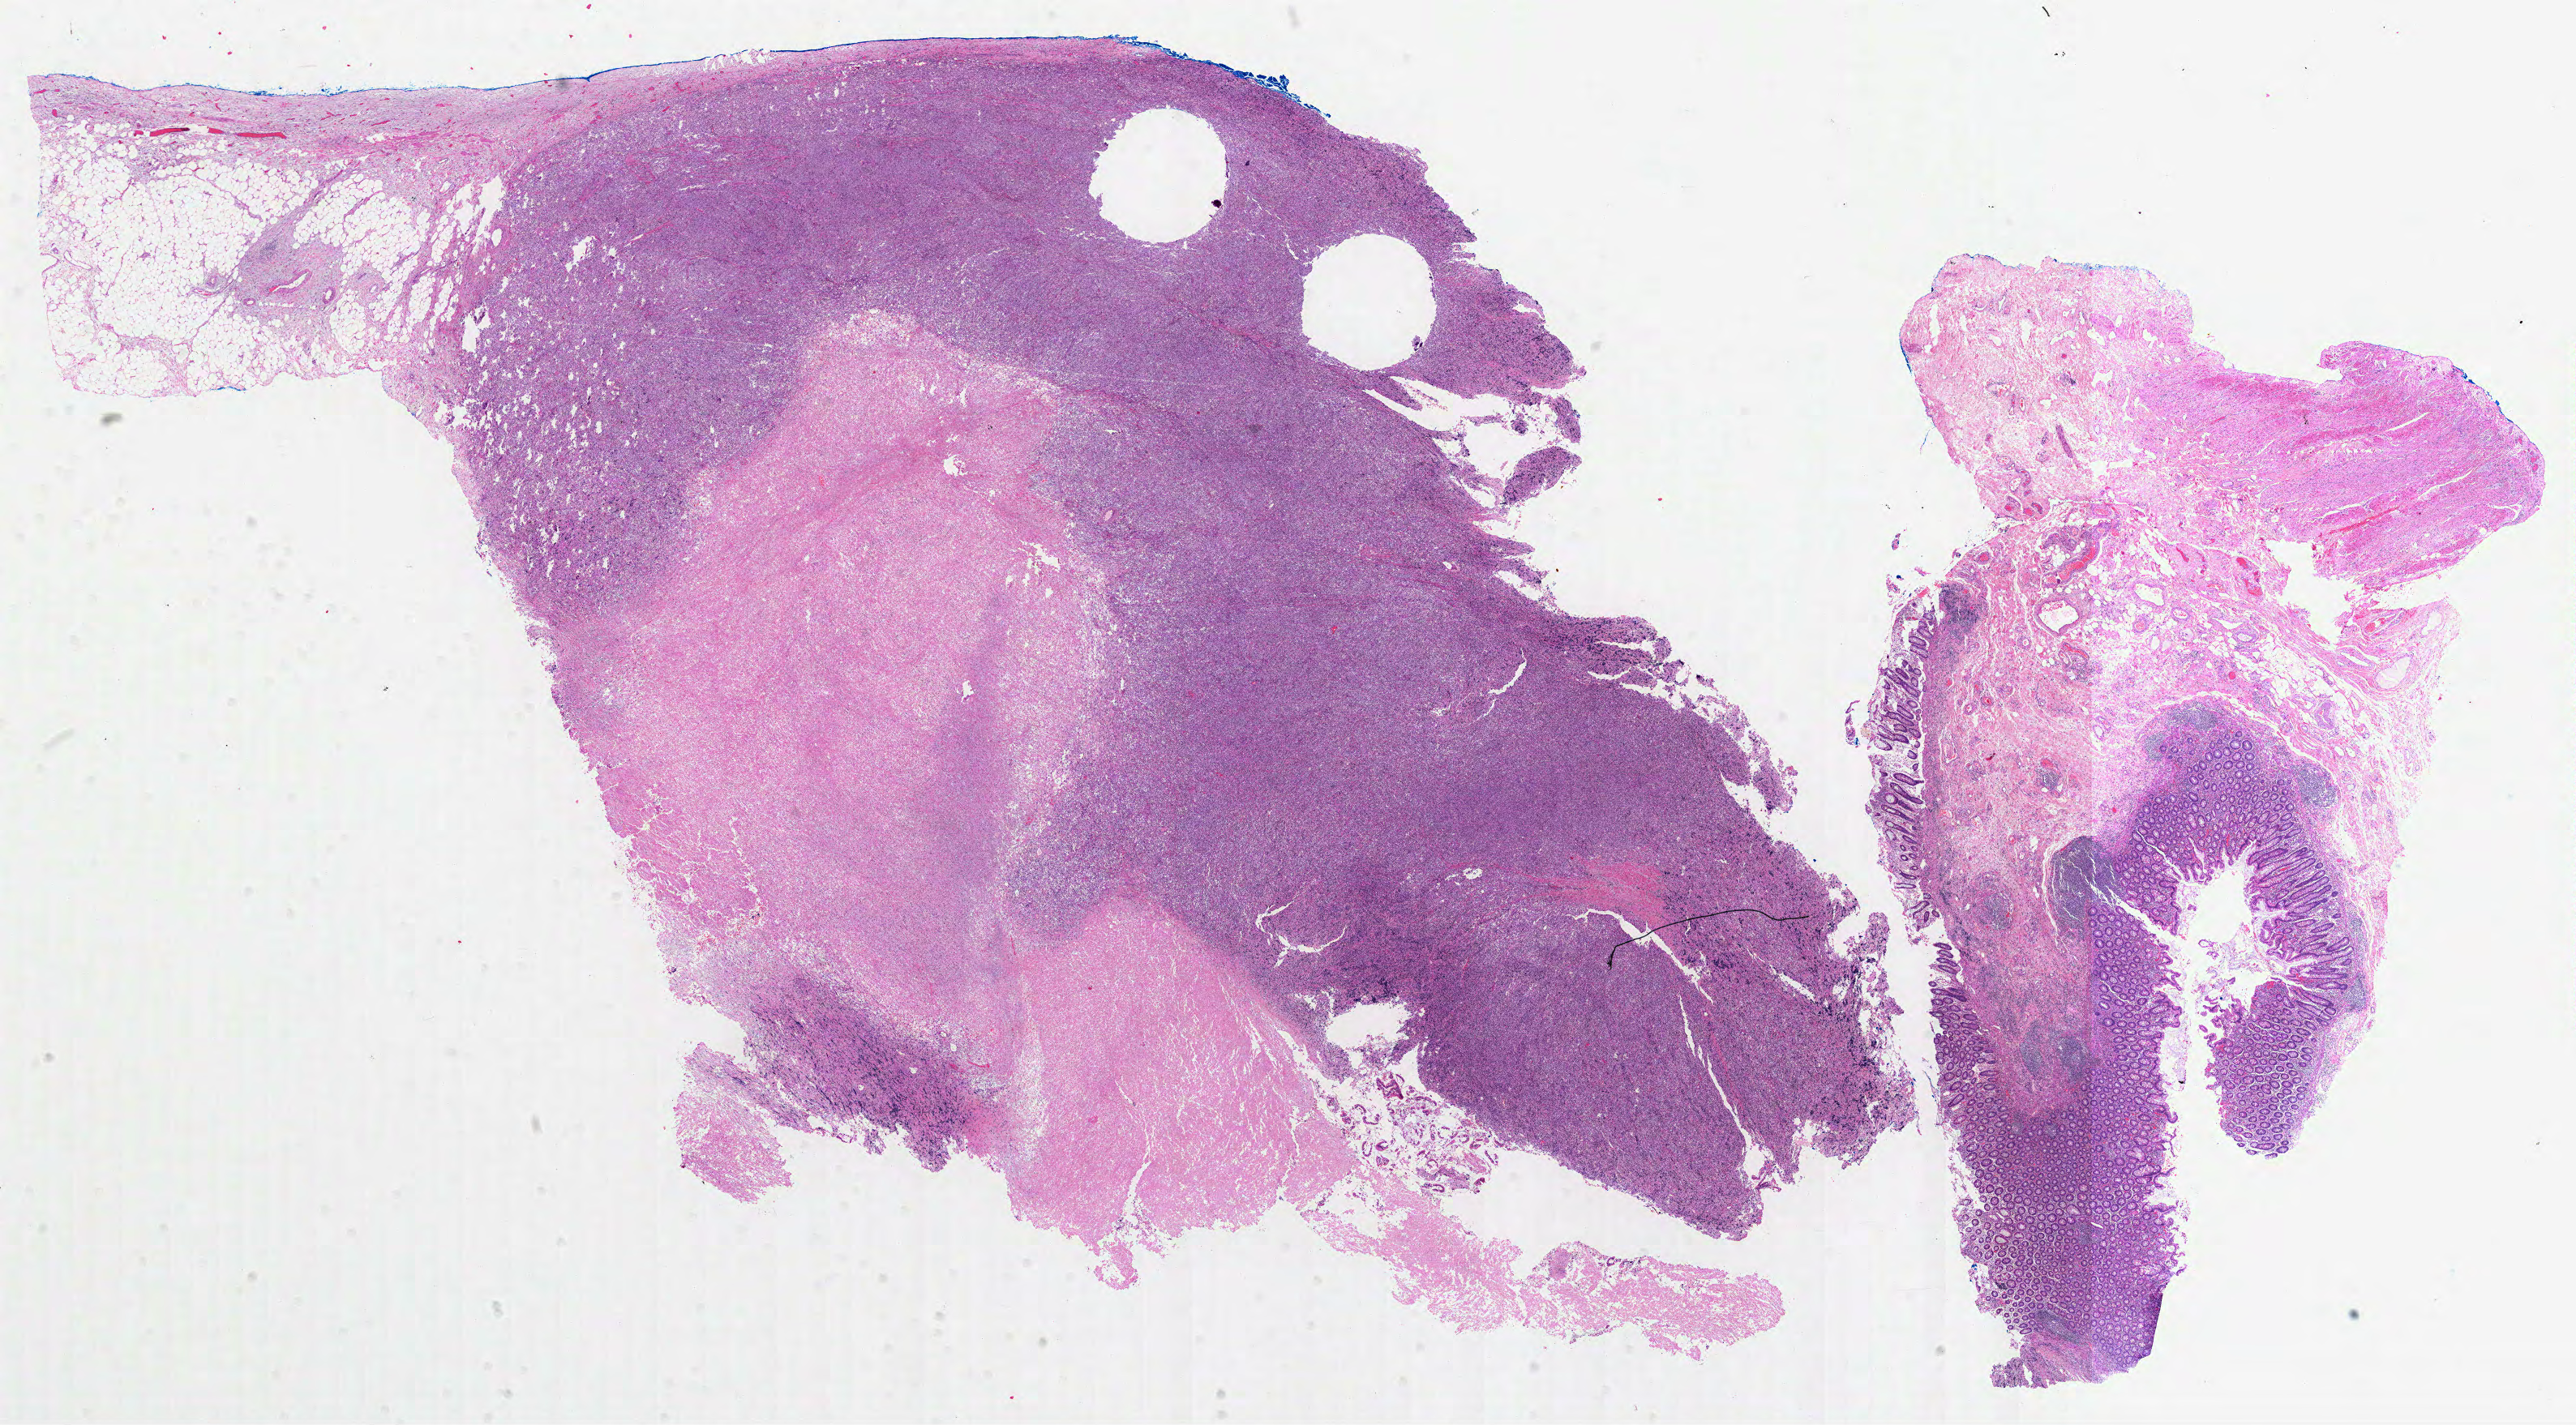
Digitized H&E tissue section (whole slide), whole scanned area (about 25.6 x 14.2 mm, from a 40x scan) shown as a low-resolution overview; formalin-fixed paraffin-embedded (FFPE) diagnostic section; sample: primary tumour, lymphoid tissue. Patient: female, age at initial diagnosis 70 years.
Diagnosis: Diffuse large B-cell lymphoma, NOS (colon, NOS).